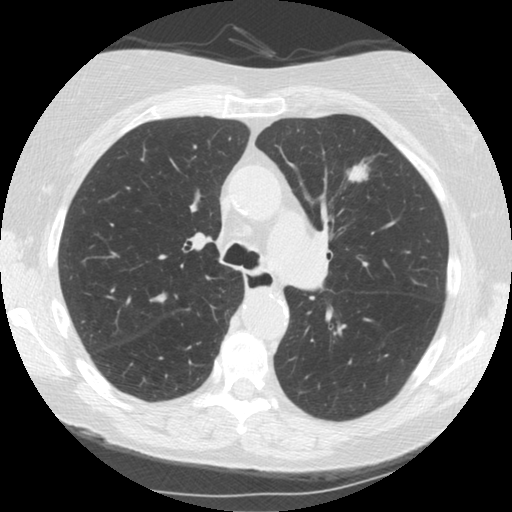
Low-dose screening chest CT, one axial slice; slice 97 of 153 in the series (ordered by position); reconstruction kernel STANDARD; 120 kVp; lung window (W 1500 / L -600 HU); 2.5 mm slice thickness; 512 × 512 image matrix, field of view 330 × 330 mm.
Structures marked on this image (manually delineated by an expert):
- lesion 1 (tumor, upper lobe of left lung): bounding box [x1, y1, x2, y2] px = [349, 159, 371, 182]